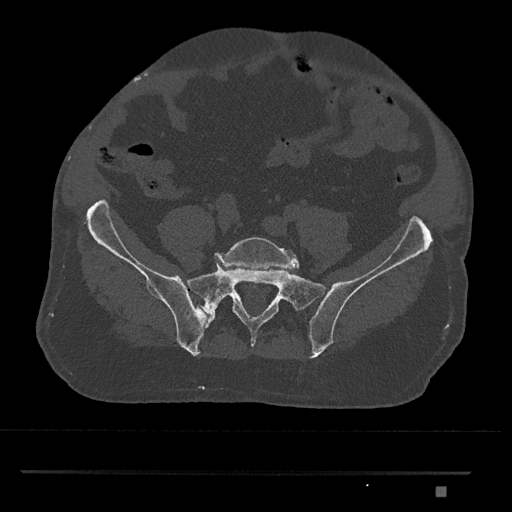
CT including the spine, one axial slice; position 518 of 1134 along the scan axis; reconstruction kernel Br40s/3; 120 kVp; bone window (W 1800 / L 400 HU); 512 × 512 image matrix, field of view 429 × 429 mm. Patient: male, 65 years. Case-level facts recorded for this patient, not image findings: primary cancer: prostate.
Structures marked on this image (semi-automatic segmentation, software-assisted and operator-edited):
- L5 vertebra: bounding box [x1, y1, x2, y2] px = [215, 237, 300, 269]